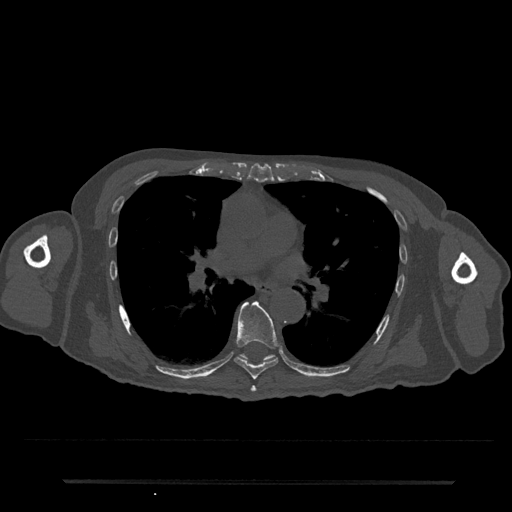
CT including the spine, one axial slice; position 469 of 797 along the scan axis; 120 kVp; bone window (W 1800 / L 400 HU); 0.5 mm slice thickness; 512 × 512 image matrix, field of view 427 × 427 mm. Male patient, age 74 years. From the clinical record (not read from this slice): primary cancer: prostate.
Structures marked on this image (semi-automatic segmentation, software-assisted and operator-edited):
- T6 vertebra: box from (x=250, y=386) to (x=256, y=392) px
- T7 vertebra: (x=234, y=301)–(x=279, y=380)
- T8 vertebra: (x=240, y=354)–(x=275, y=361)